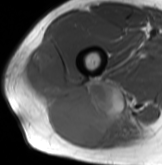
MRI of an extremity soft-tissue mass, one axial slice; MR volume resampled by the dataset authors to the PET/CT grid (not the native acquisition matrix); 3.27 mm slice thickness; 162 × 165 image matrix, field of view 158 × 161 mm. Male patient. From the clinical record (not read from this slice): histological type: poorly differentiated synovial sarcoma; grade: high; site of the primary tumour: right buttock.
Structures marked on this image (expert contour drawn on MRI and transferred to this co-registered scan by the dataset authors):
- gross tumour volume including surrounding oedema: bounding box <23,40,140,146> (left, top, right, bottom; pixels)
- gross tumour volume (mass): <23,40,126,146>